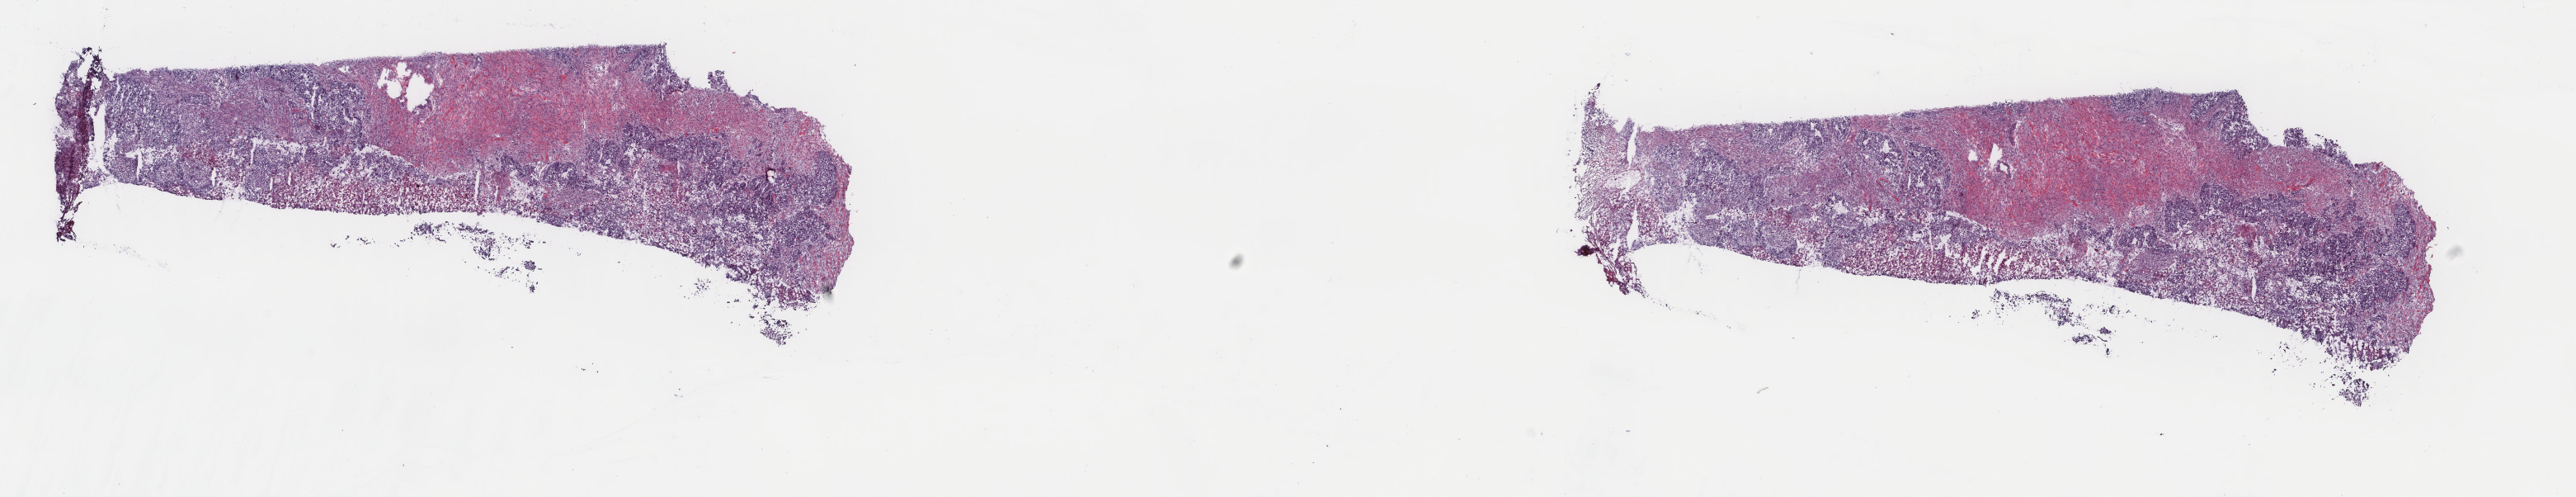
Whole-slide histology image, Hematoxylin and eosin (H&E) stained — a low-resolution overview of the entire scanned area, about 24.8 x 4.8 mm (acquisition: 40x scan); frozen section from the top of the tissue portion; sample: recurrent tumour, uterus. Female patient; age at initial diagnosis 74 years. Pathologist review of this section (percent, as recorded): tumour cells 40%, tumour nuclei 65%, normal cells 40%, stromal cells 0%, necrosis 20%. Inflammatory infiltration, as recorded: lymphocyte infiltration 3%, monocyte infiltration 0%, neutrophil infiltration 0%.
* this section: recurrent tumour
* patient diagnosis: Endometrioid adenocarcinoma, NOS (endometrium)